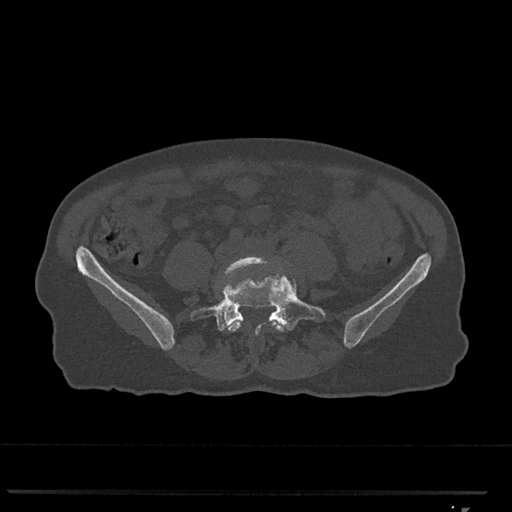
CT including the spine, one axial slice. Bone window (W 1800 / L 400 HU). 512 × 512 image matrix, field of view 380 × 380 mm. Female patient, age 62 years. From the clinical record (not read from this slice): primary cancer: renal.
Outlined on this slice (semi-automatic segmentation, software-assisted and operator-edited):
- L4 vertebra: bounding box [x1, y1, x2, y2] px = [217, 255, 285, 332]
- L5 vertebra: [190, 261, 326, 334]